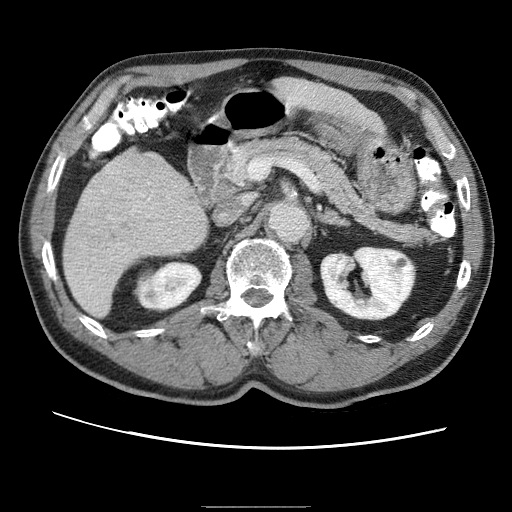
Contrast-enhanced abdominal CT (liver protocol), one axial slice. Position 19 of 75 along the scan axis. Reconstruction kernel STANDARD. 120 kVp. One of 2 acquisitions stored at this slice position. Soft-tissue window (W 400 / L 40 HU). 512 × 512 image matrix, field of view 360 × 360 mm. Case-level facts recorded for this patient, not image findings: diagnosis: hepatocellular carcinoma (patient treated with transarterial chemoembolisation; whether this scan precedes or follows treatment is not stated here); TNM stage (as recorded): Stage-II; Child-Pugh class: A; tumour differentiation: well differentiated; tumour nodularity: multinodular.
Annotated regions visible in this slice (semi-automatically segmented with operator editing):
- liver parenchyma outside the tumour (the mass and vessels are separate outlines, so this box may not span the whole liver): box from (x=64, y=152) to (x=200, y=314) px
- liver vessels: (x=102, y=163)–(x=116, y=190)